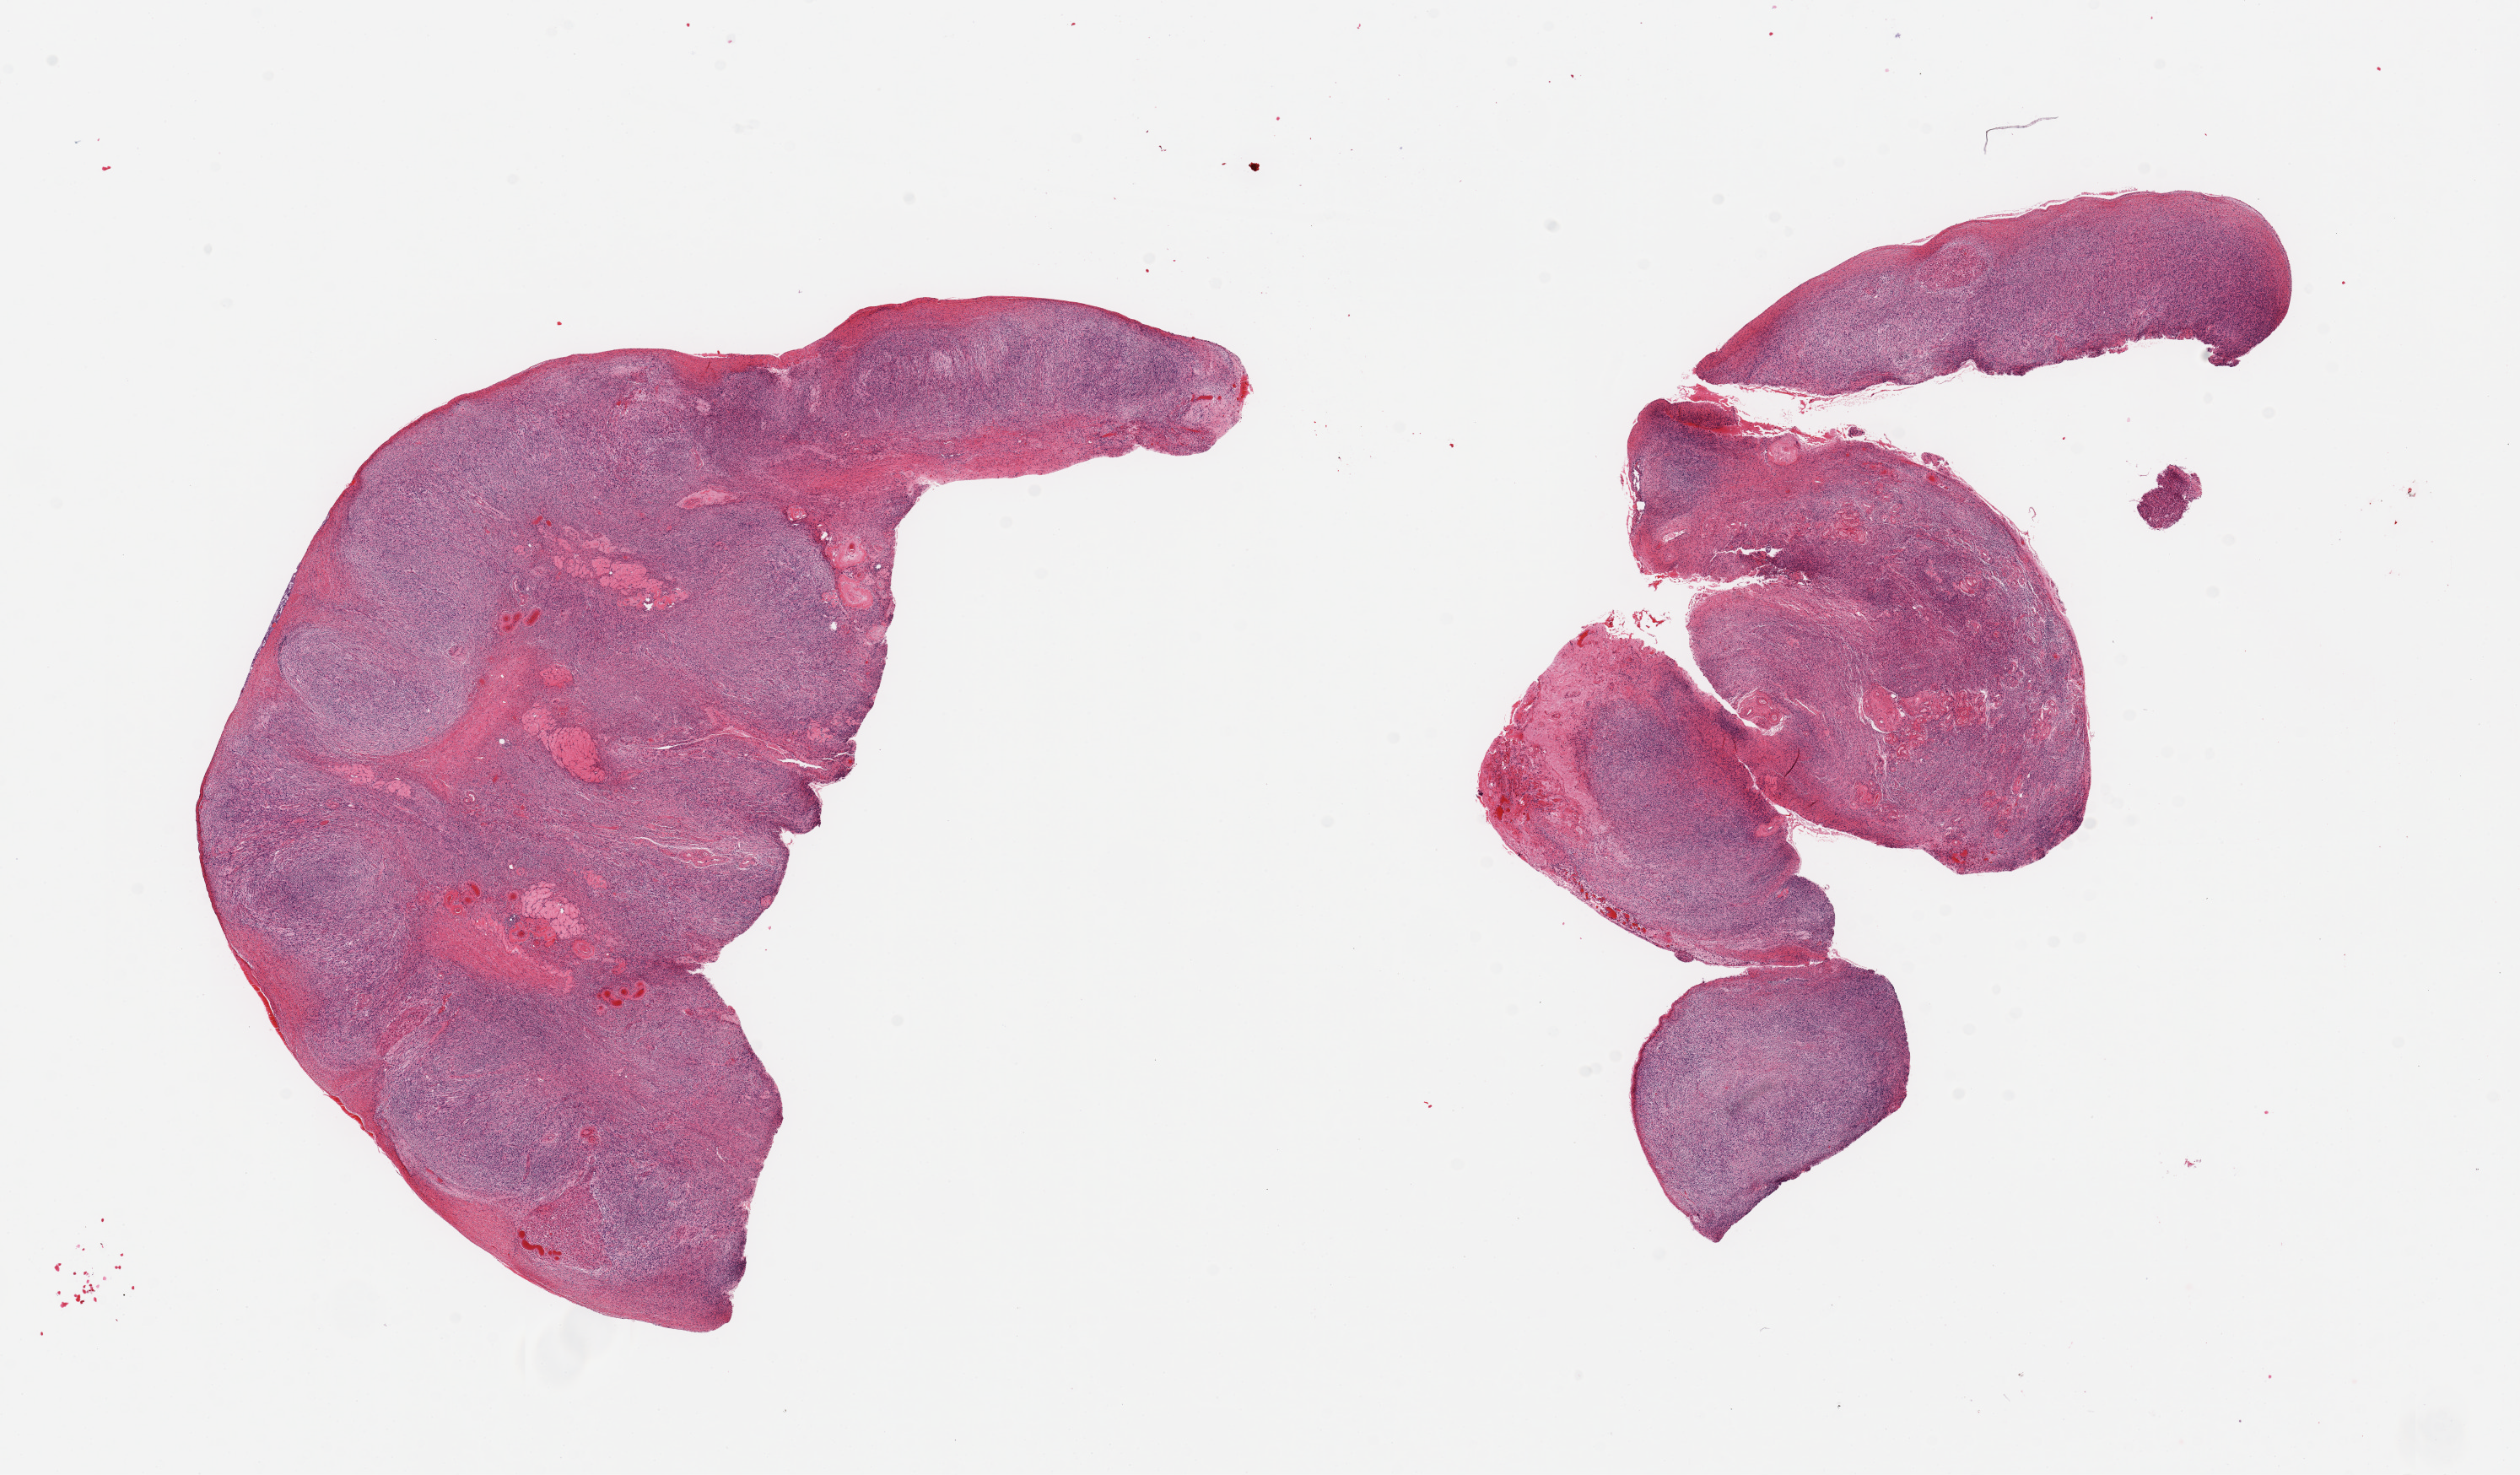
Digitized haematoxylin and eosin-stained section — a low-resolution overview of the entire scanned area, about 23.6 x 13.8 mm; PAXgene-fixed, paraffin-embedded tissue; sampled site (target tissue): ovary; tissue donor sample.
• reviewer comment on this tissue sample: 6 partially fragmented pieces; atrophic; rare corpora albicantia